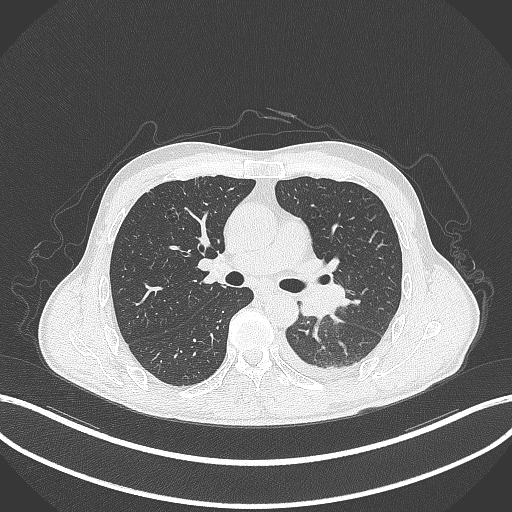
Chest CT, one axial slice; position 194 of 295 along the scan axis; reconstruction kernel B70f; lung window (W 1500 / L -600 HU); 1 mm slice thickness; 512 × 512 image matrix, field of view 400 × 400 mm. Male patient, age 47 years. Case-level facts recorded for this patient, not image findings: clinical TNM (as recorded): T3 N1 M1c; histopathological grade: G3.
Annotated regions visible in this slice (rectangle marked by the reading radiologist):
- lung tumour (recorded histology: small cell carcinoma): bounding box (x1, y1, x2, y2) in pixels: (296, 283, 349, 319)